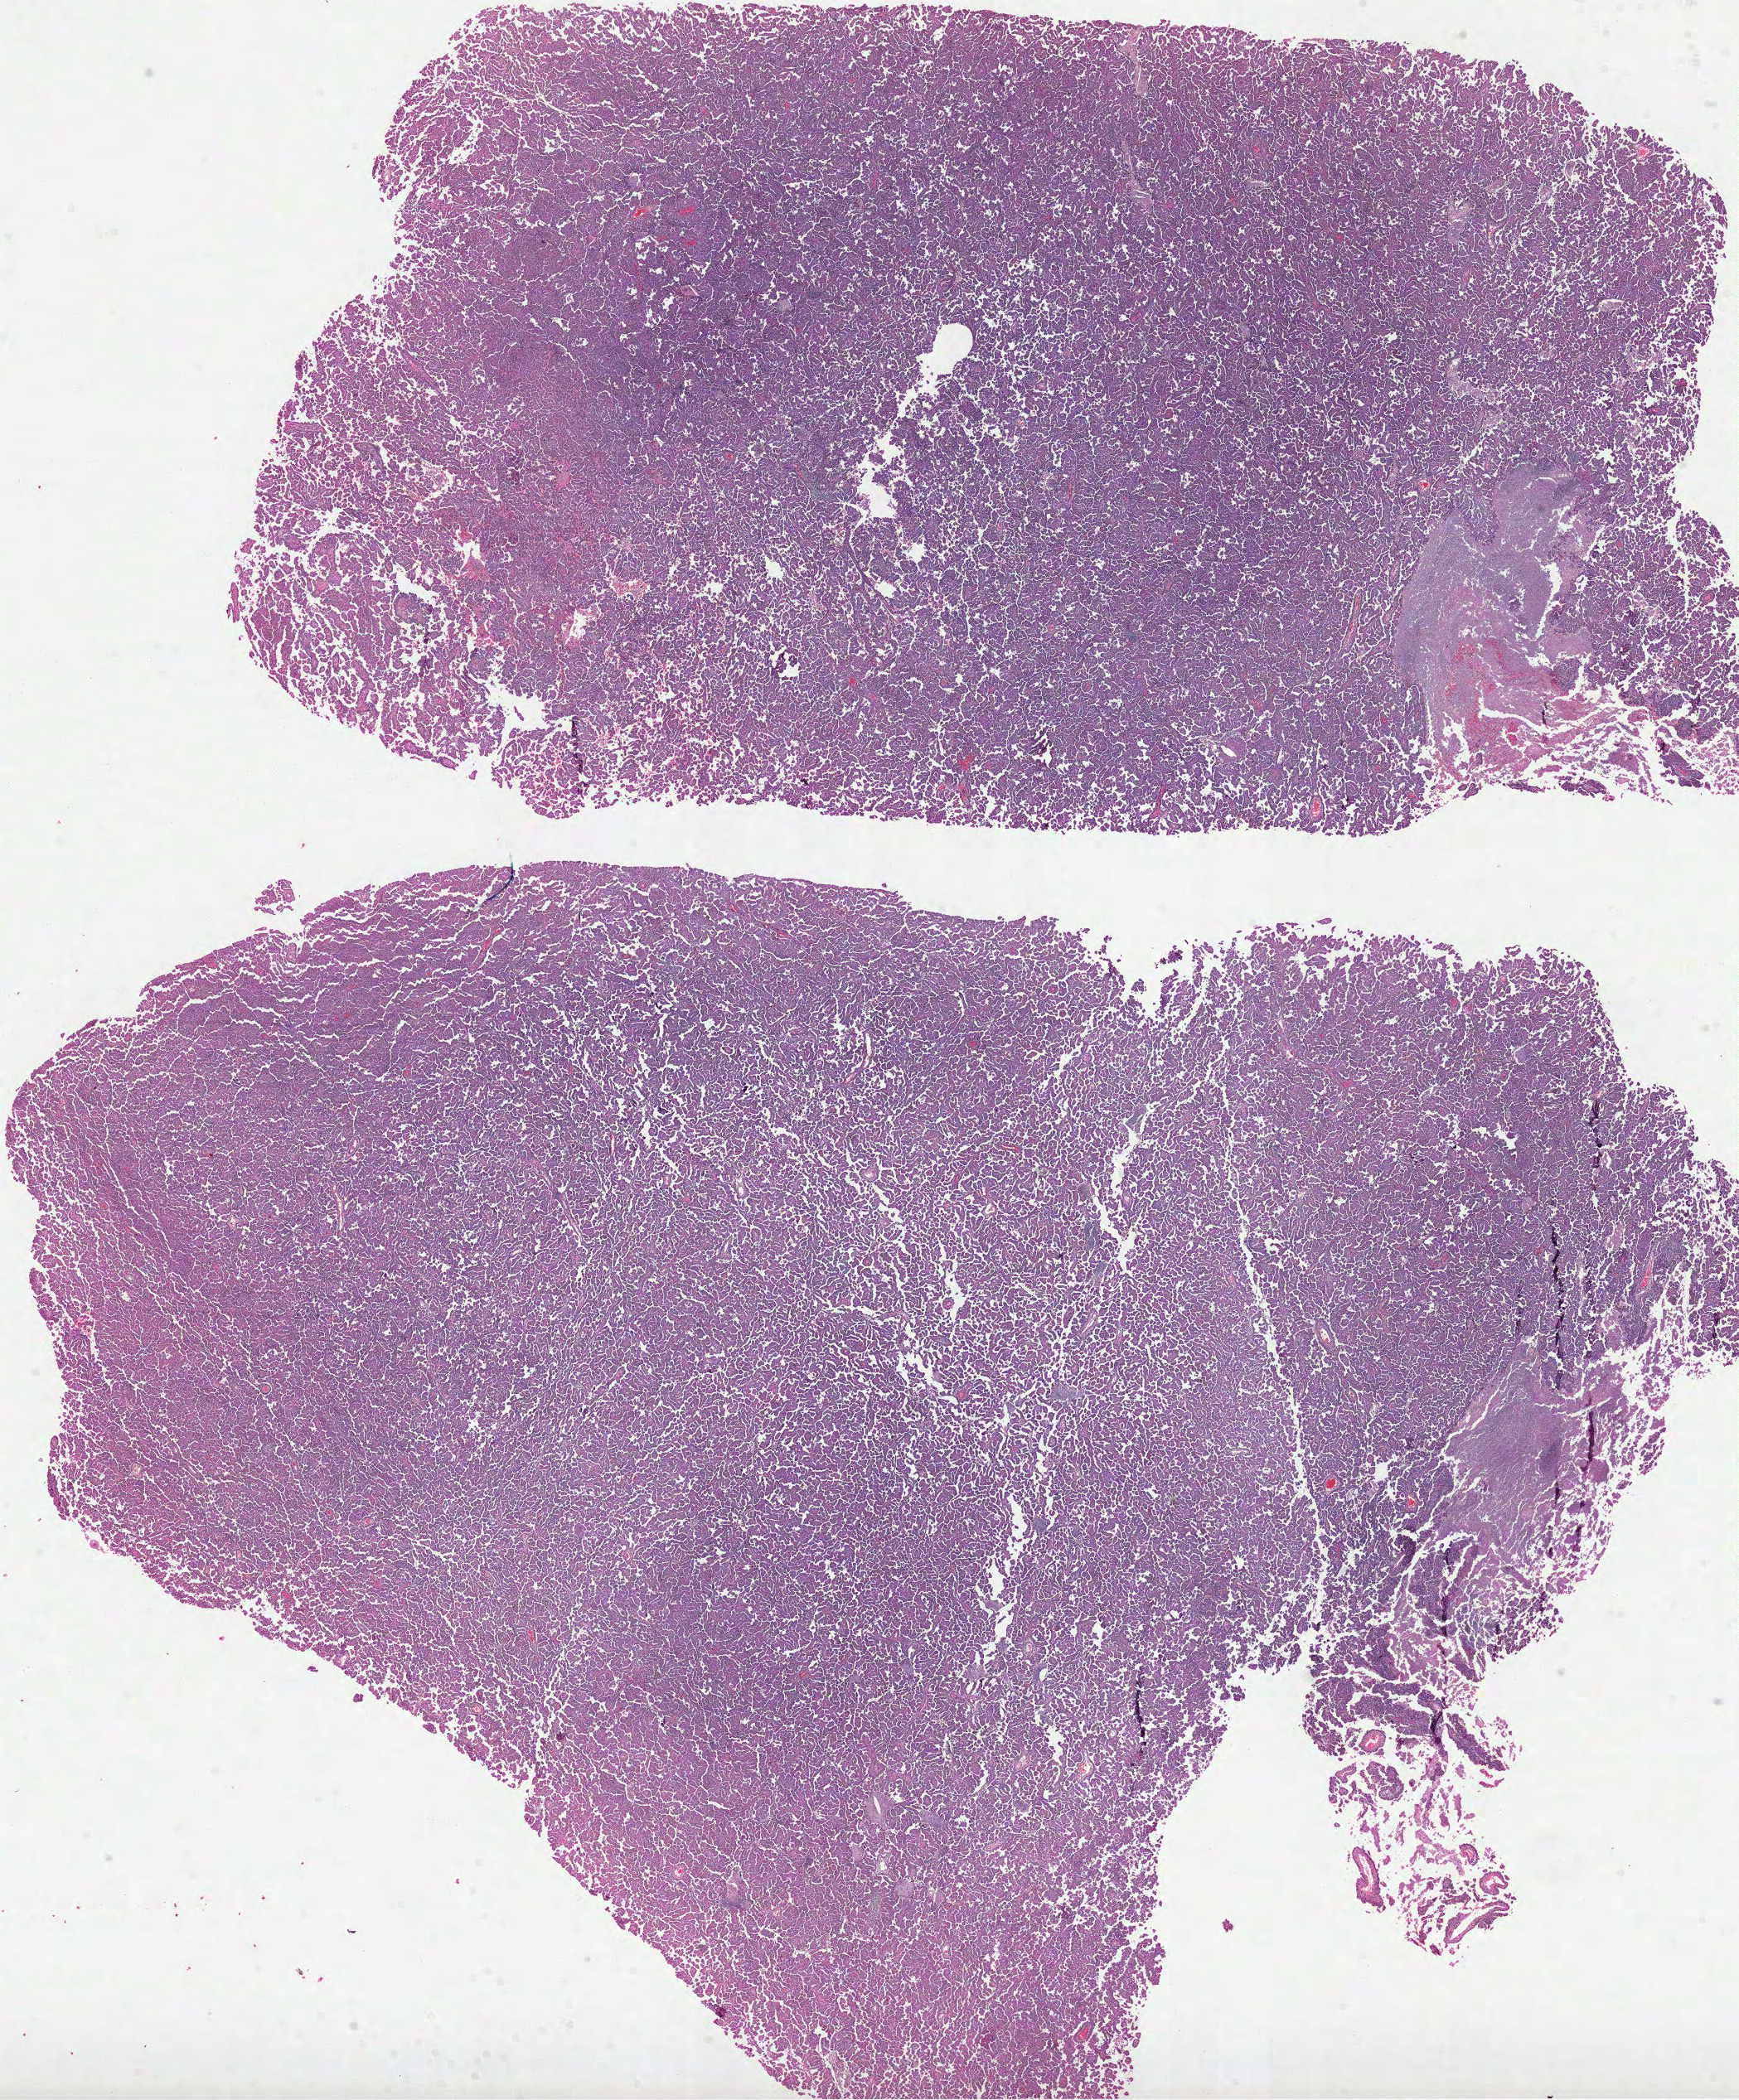
H&E whole-slide image, whole scanned area (about 16.9 x 20.4 mm, from a 40x scan) shown as a low-resolution overview; formalin-fixed paraffin-embedded (FFPE) diagnostic section; sample: primary tumour, kidney. Patient: female, age at initial diagnosis 75 years.
- laterality: left
- histologic diagnosis: Papillary adenocarcinoma, NOS